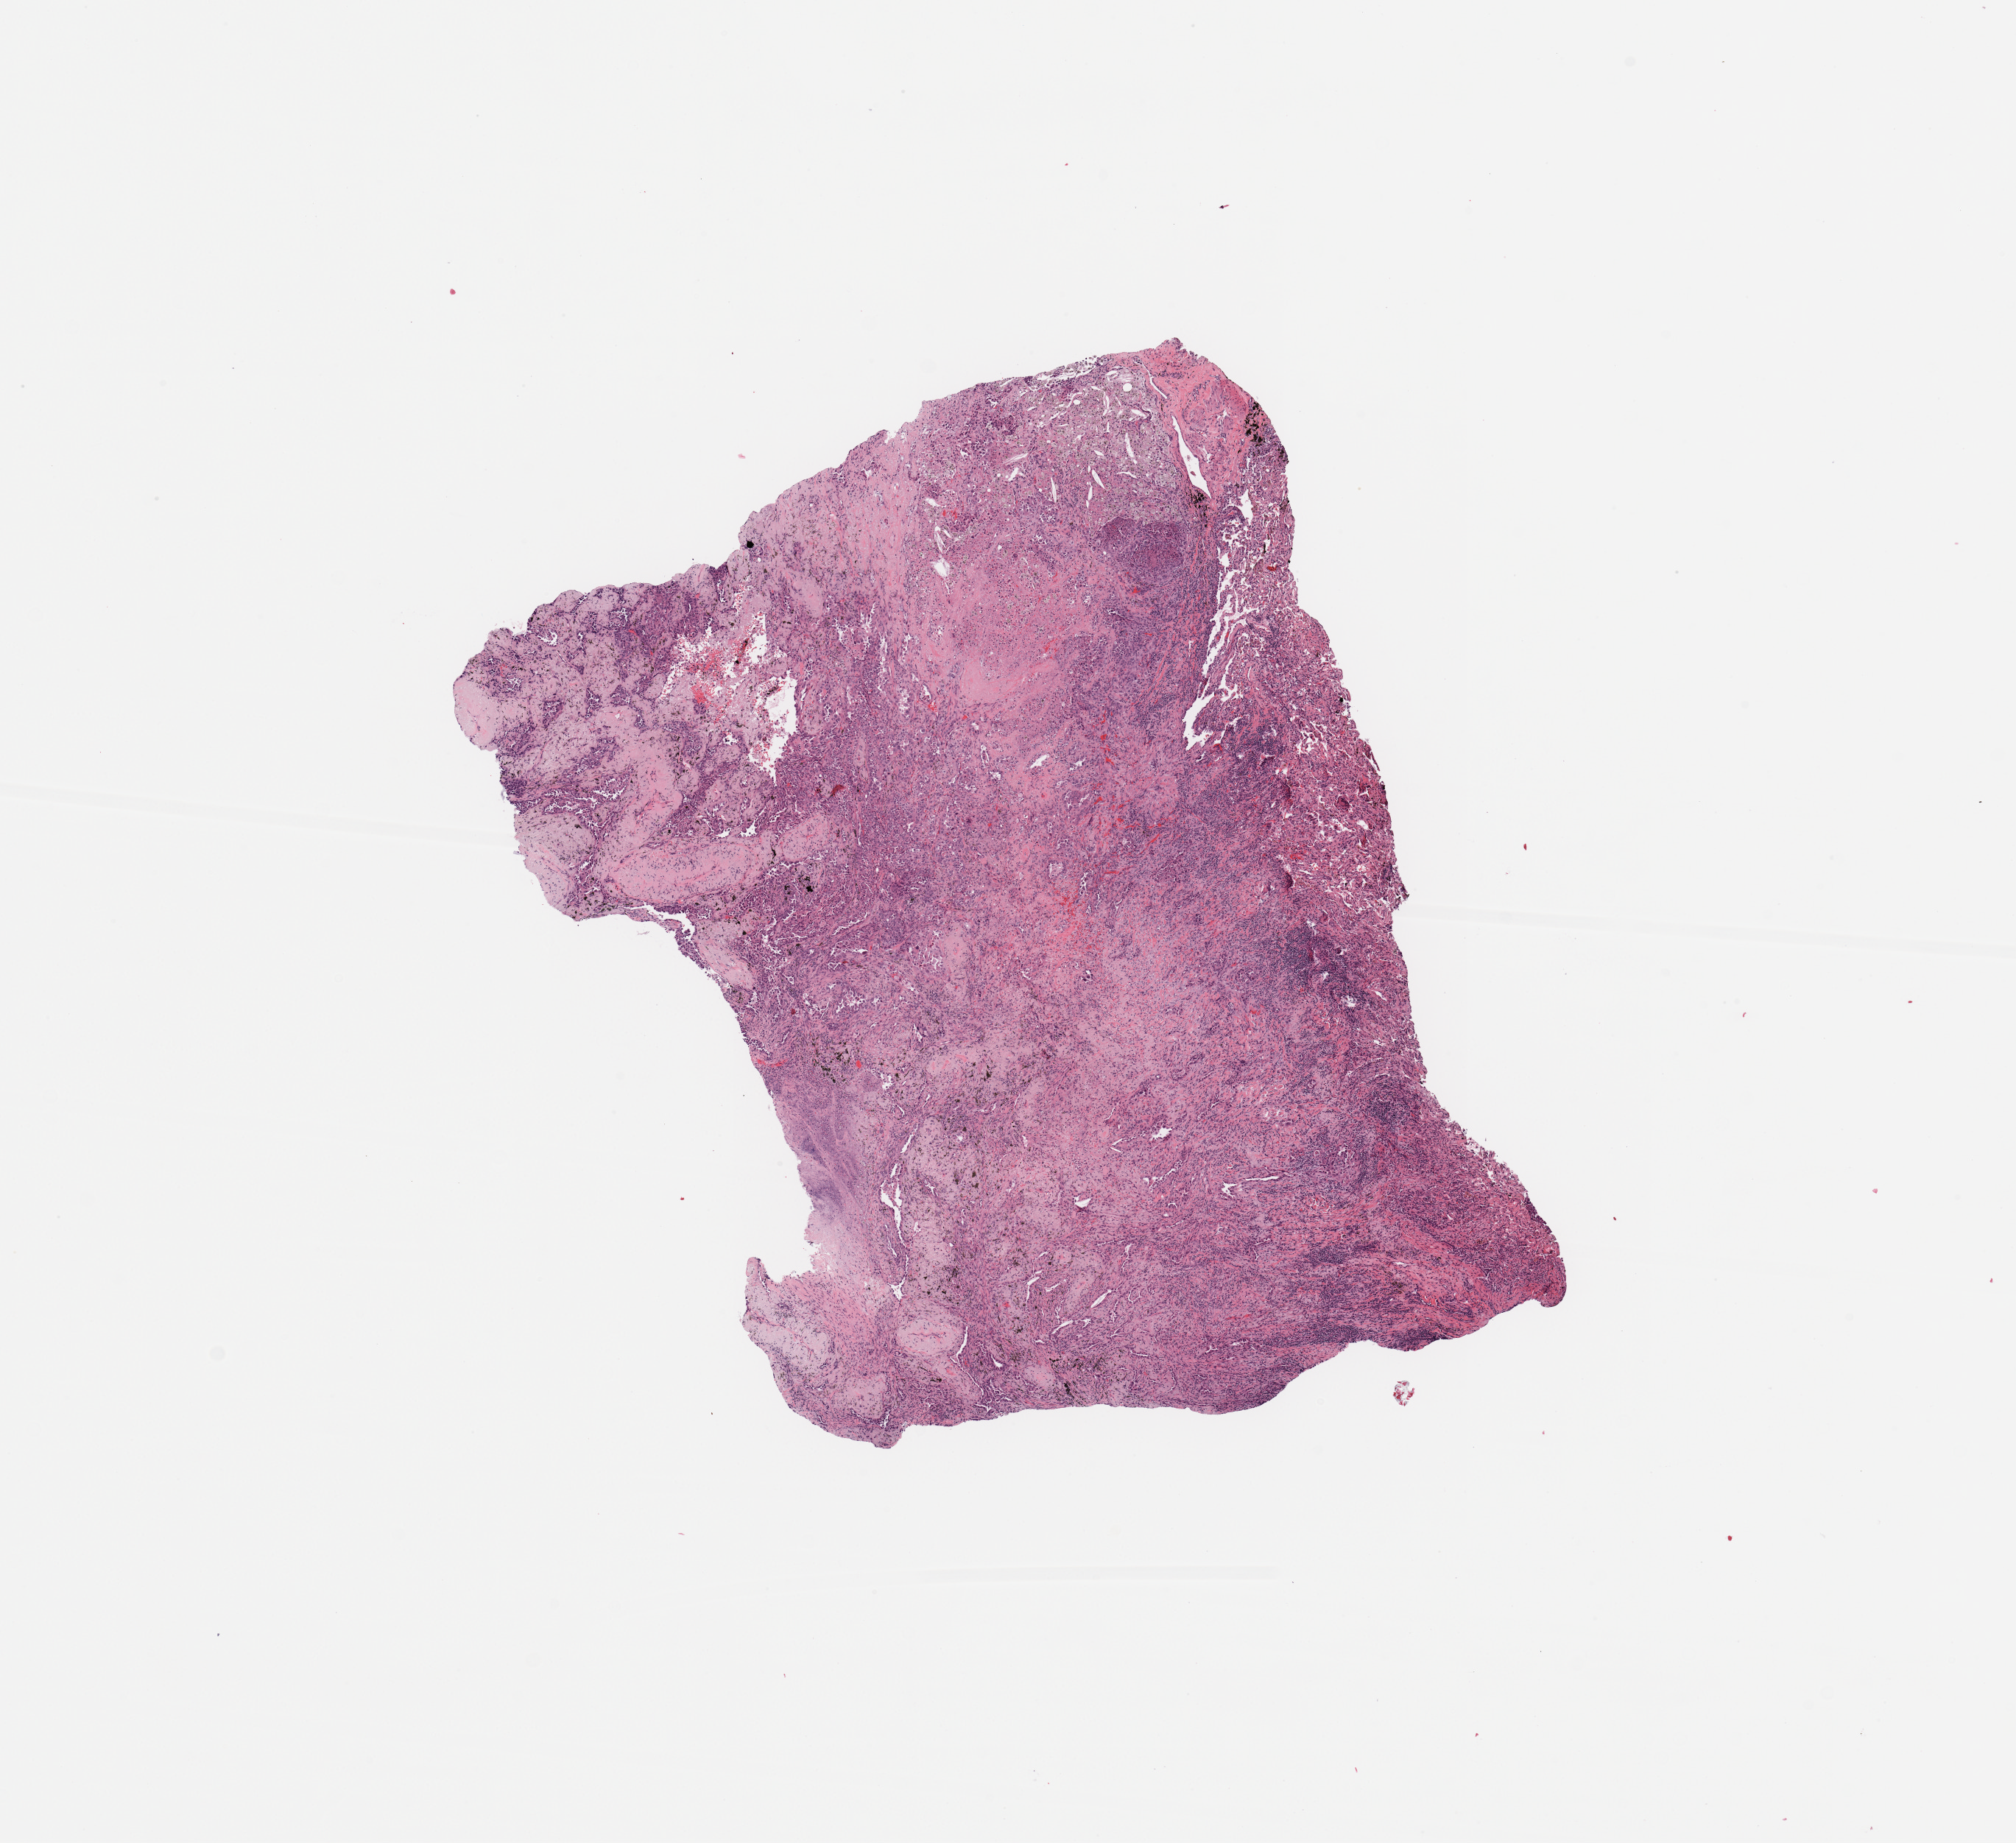
Whole-slide histology image, H&E — low-resolution overview of the scanned area, about 10.8 x 9.9 mm. Tumour tissue sample, lung. Patient: male, age 61 years. Histologic grade: G3 (poorly differentiated).
Histologic diagnosis: Adenocarcinoma, NOS. AJCC pathologic stage: IIIA.